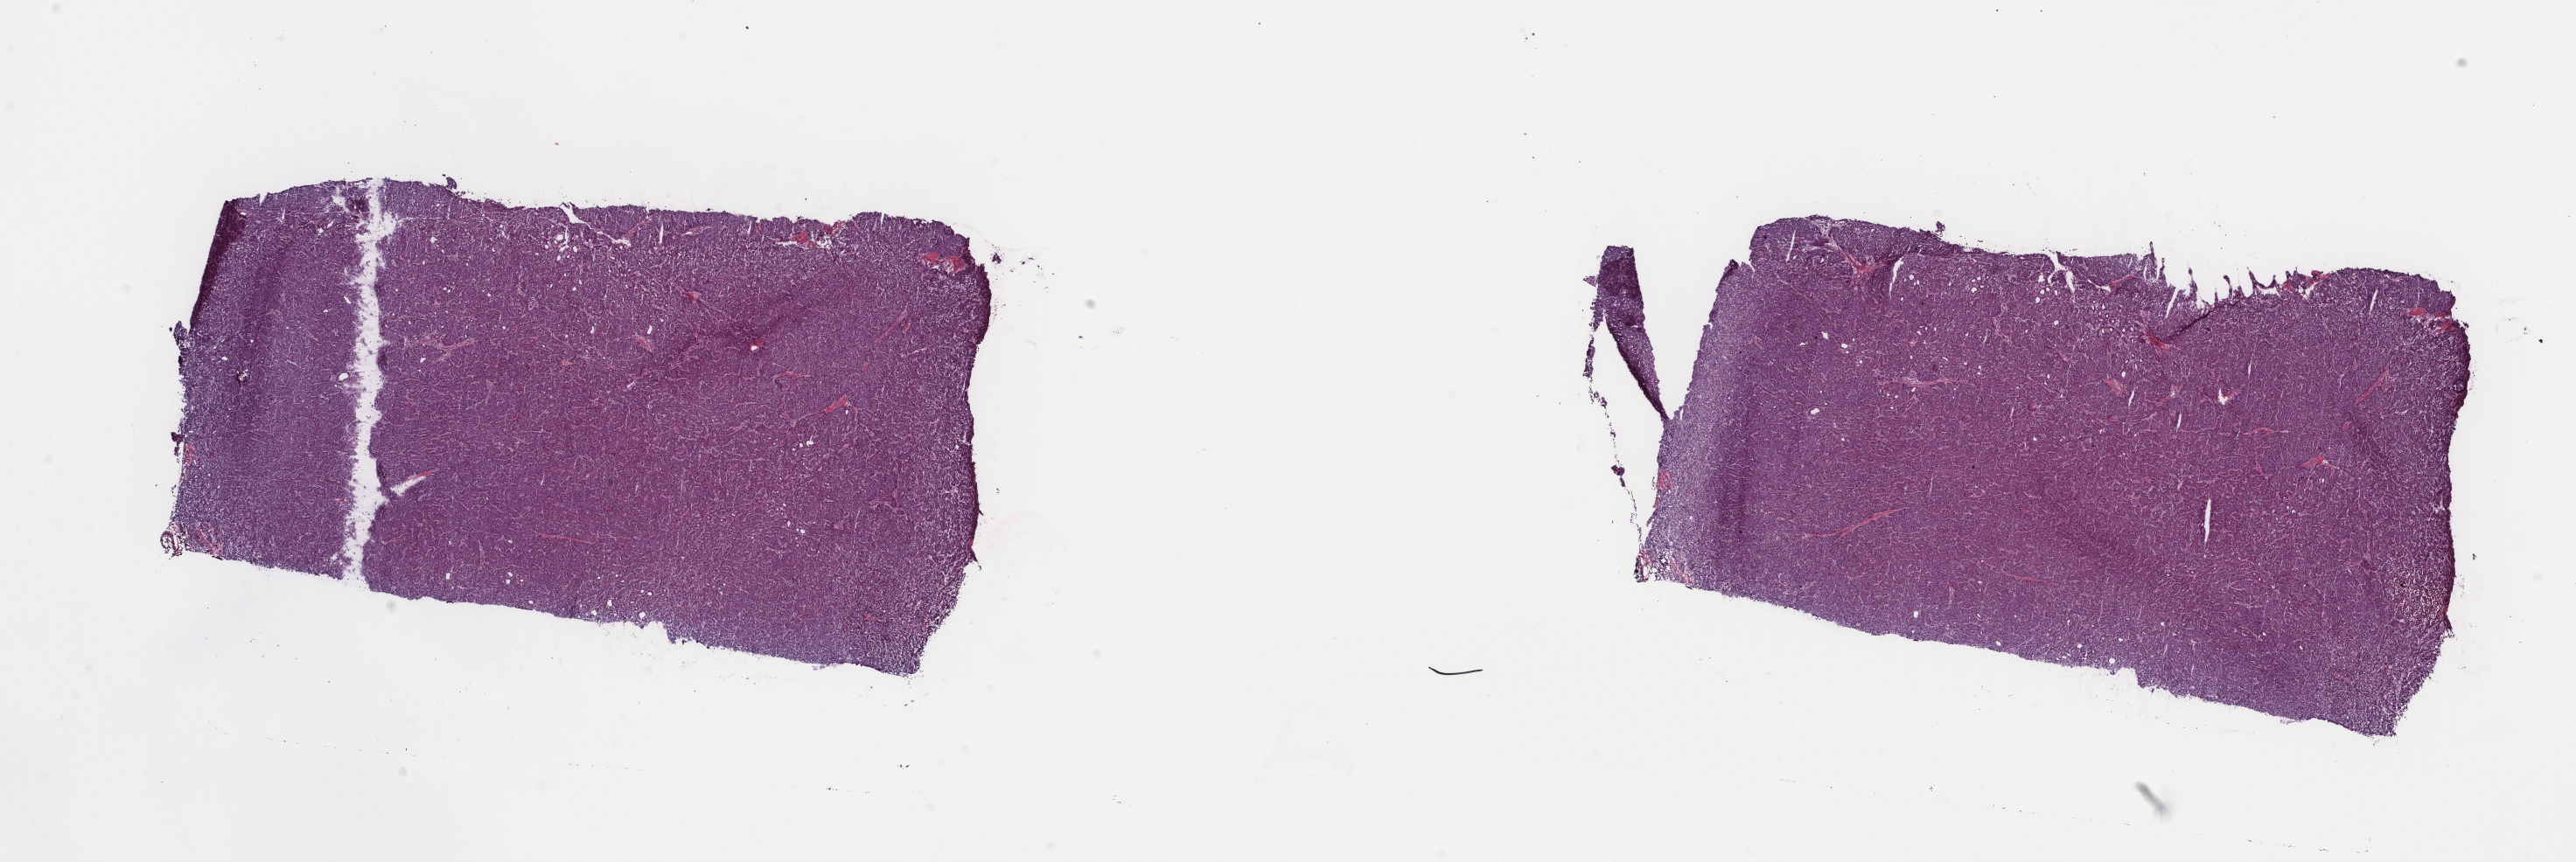
Digitized H&E-stained tissue section (whole slide), whole scanned area (about 23.4 x 7.8 mm) shown as a low-resolution overview, frozen section, primary tumour sample from the liver. Male patient; age at initial diagnosis 65 years. Histologic grade: G1 (well differentiated). Pathologist review of this section (percent, as recorded): tumour cells 100%, tumour nuclei 80%, normal cells 0%, stromal cells 0%, necrosis 0%. Infiltration values recorded for this section: lymphocyte infiltration 2%, monocyte infiltration 0%, neutrophil infiltration 0%.
AJCC pathologic stage: I (6th edition). Histologic diagnosis: Hepatocellular carcinoma, NOS.